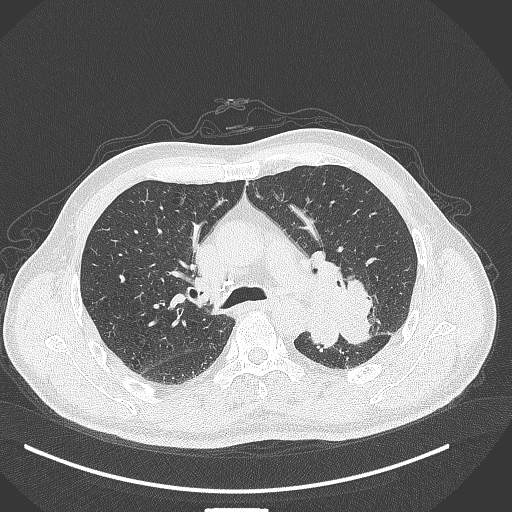
Chest CT, one axial slice; slice 276 of 429 in the series (ordered by position); 120 kVp; lung window (W 1500 / L -600 HU); 512 × 512 image matrix, field of view 400 × 400 mm. Patient: male, 55 years. Case-level facts recorded for this patient, not image findings: clinical TNM (as recorded): T3 N0 M1c; histopathological grade: G3.
Structures marked on this image (bounding box drawn by a radiologist):
- lung tumour (recorded histology: adenocarcinoma): bounding box <307,254,376,354> (left, top, right, bottom; pixels)